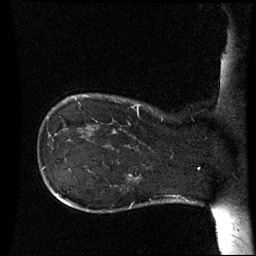
Breast MRI (dynamic contrast-enhanced), one sagittal slice; slice 10 of 60 in the series (ordered by position); dynamic contrast-enhanced series, image 2 of 3 at this slice position (ordered by acquisition); 1.5 T; TE 4.2 ms, TR 8.9 ms; 256 × 256 image matrix, field of view 230 × 230 mm. Patient: female, 42 years. From the clinical record (not read from this slice): setting: breast cancer imaged before/during neoadjuvant chemotherapy; receptor status: HER2-positive.
Annotated regions visible in this slice (semi-automatically segmented with operator editing):
- analysis volume of interest (the breast-tissue region the enhancement analysis was run in; not a lesion): bounding box (x1, y1, x2, y2) in pixels: (106, 102, 173, 150)
- tumour enhancement mask (voxels above the 70 % enhancement threshold inside the analysis volume of interest): (136, 104, 138, 112)